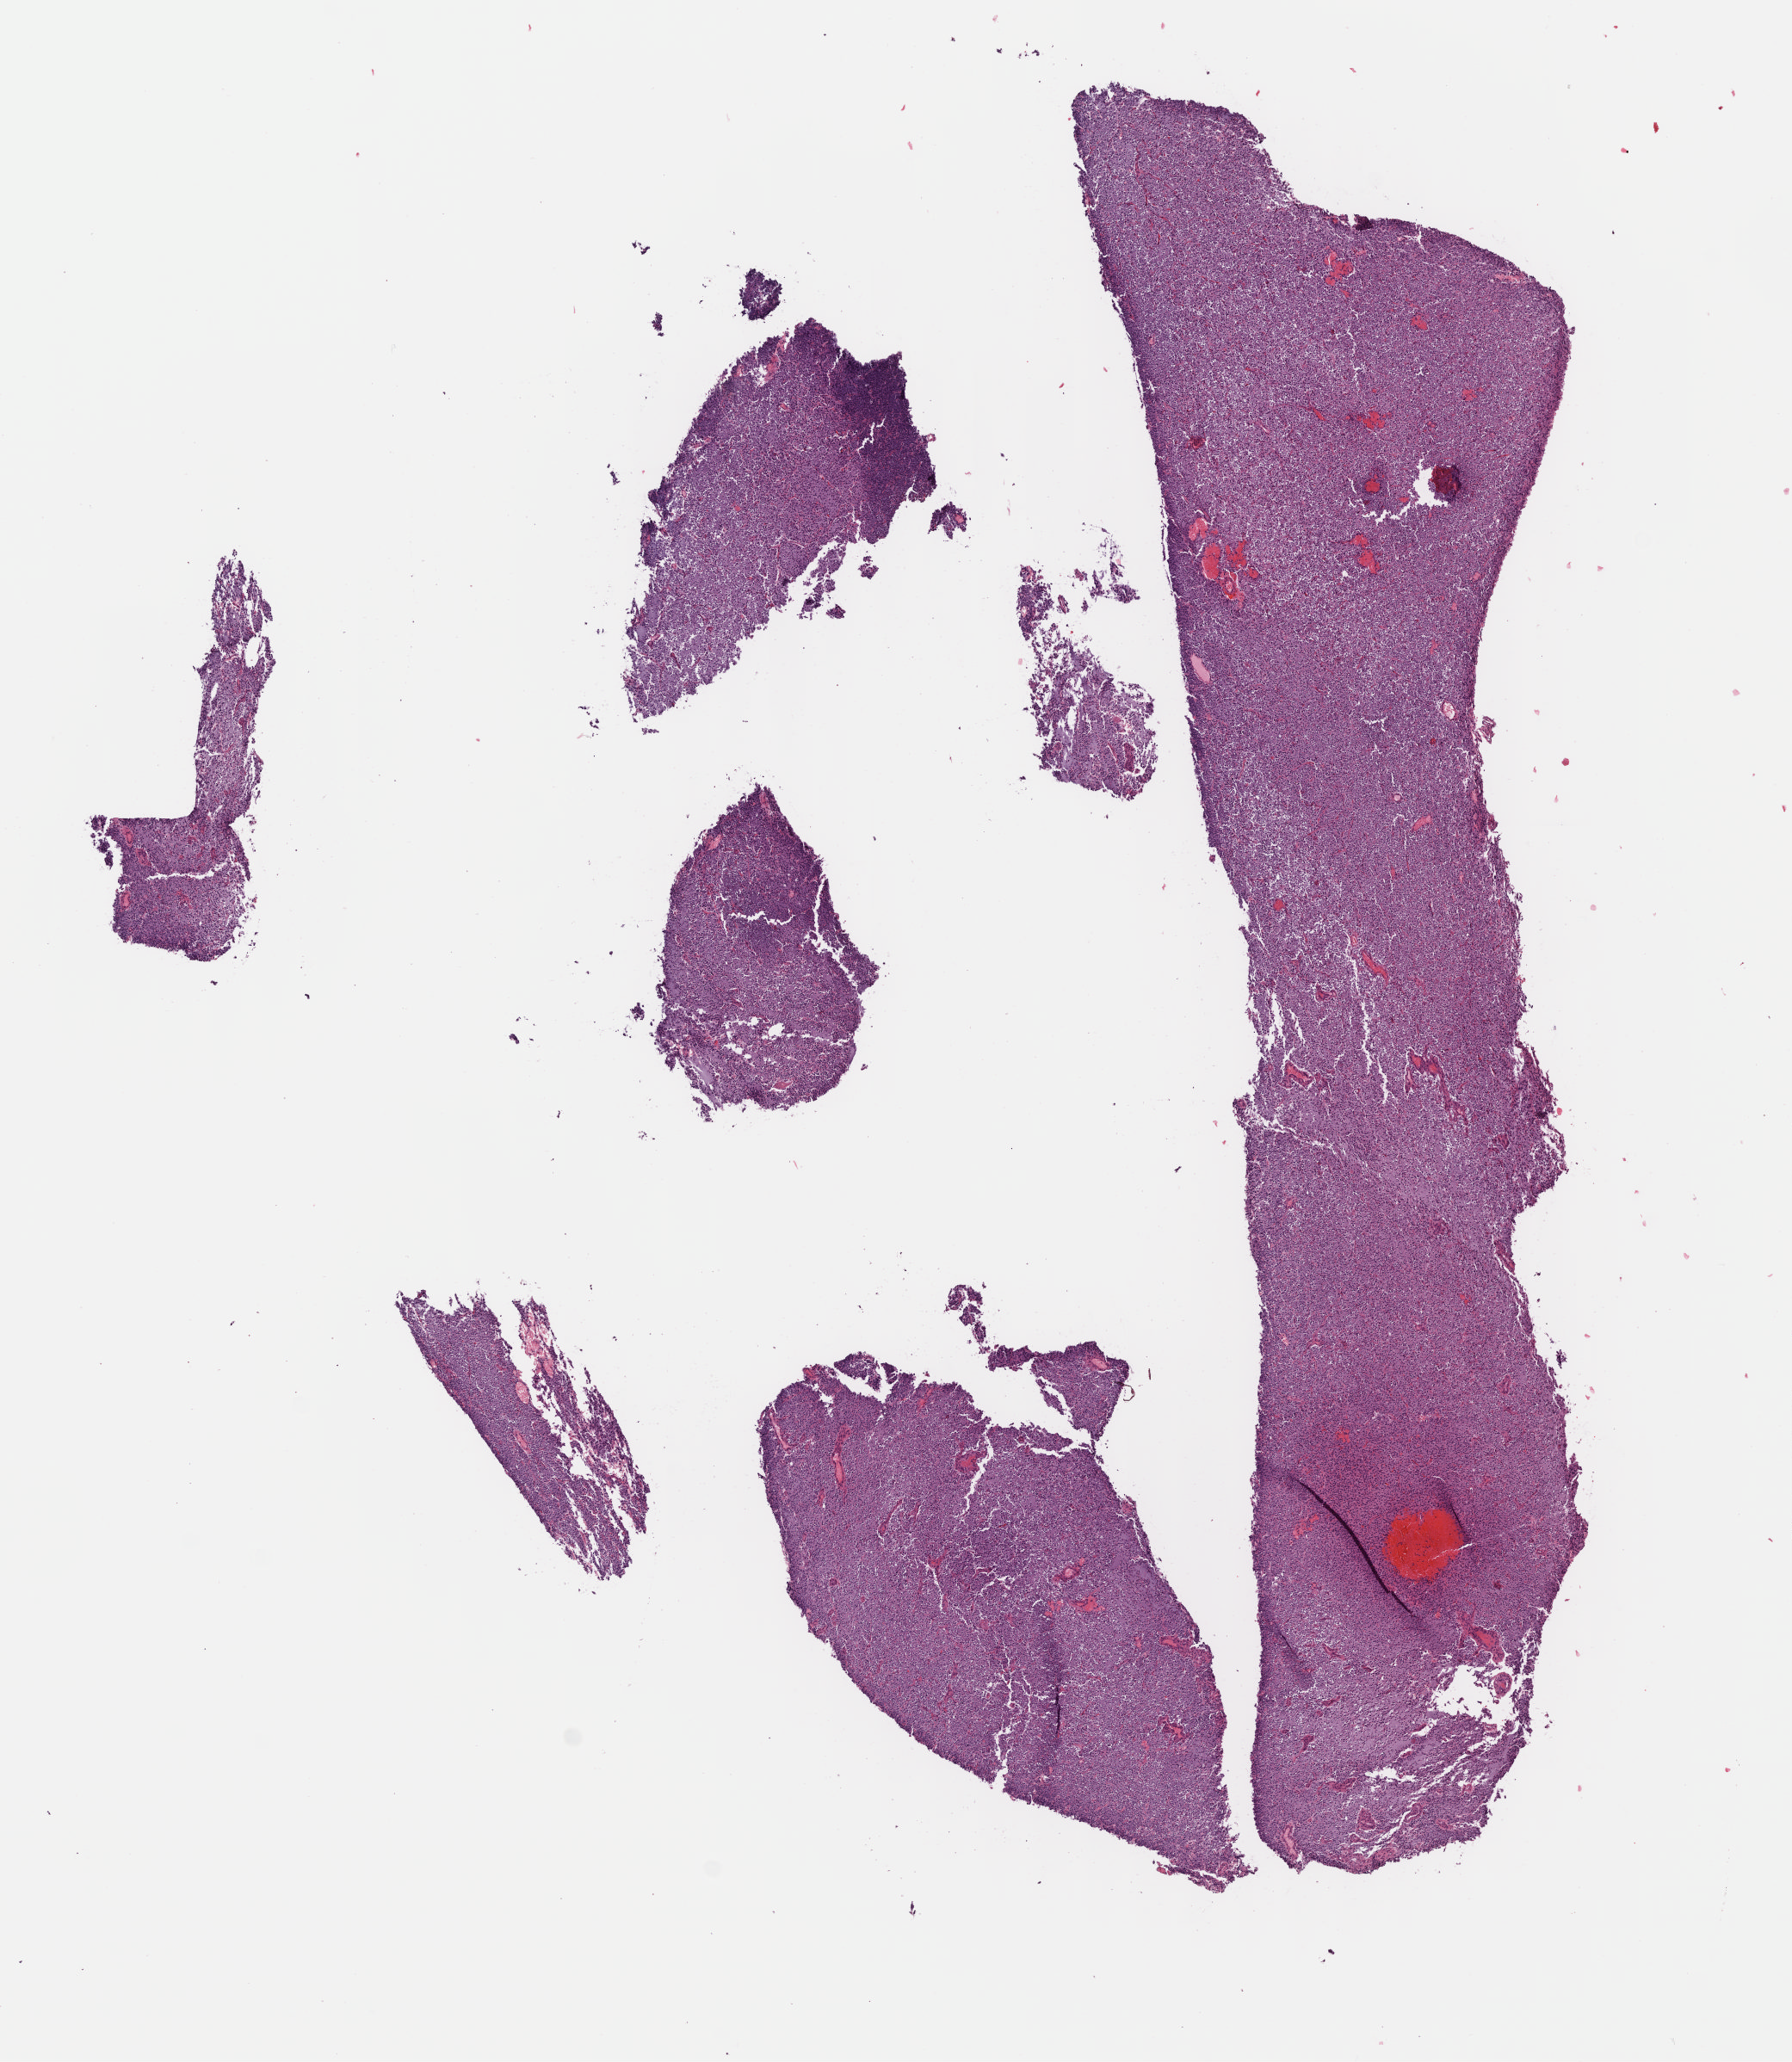
H&E whole-slide image — low-resolution overview of the scanned area, about 8.2 x 9.4 mm (slide scanned at 40x); FFPE section; brain, primary tumour sample. Male, age 30 years at initial diagnosis. Histologic grade: G3 (poorly differentiated).
Histologic diagnosis: Oligodendroglioma, anaplastic (cerebrum).